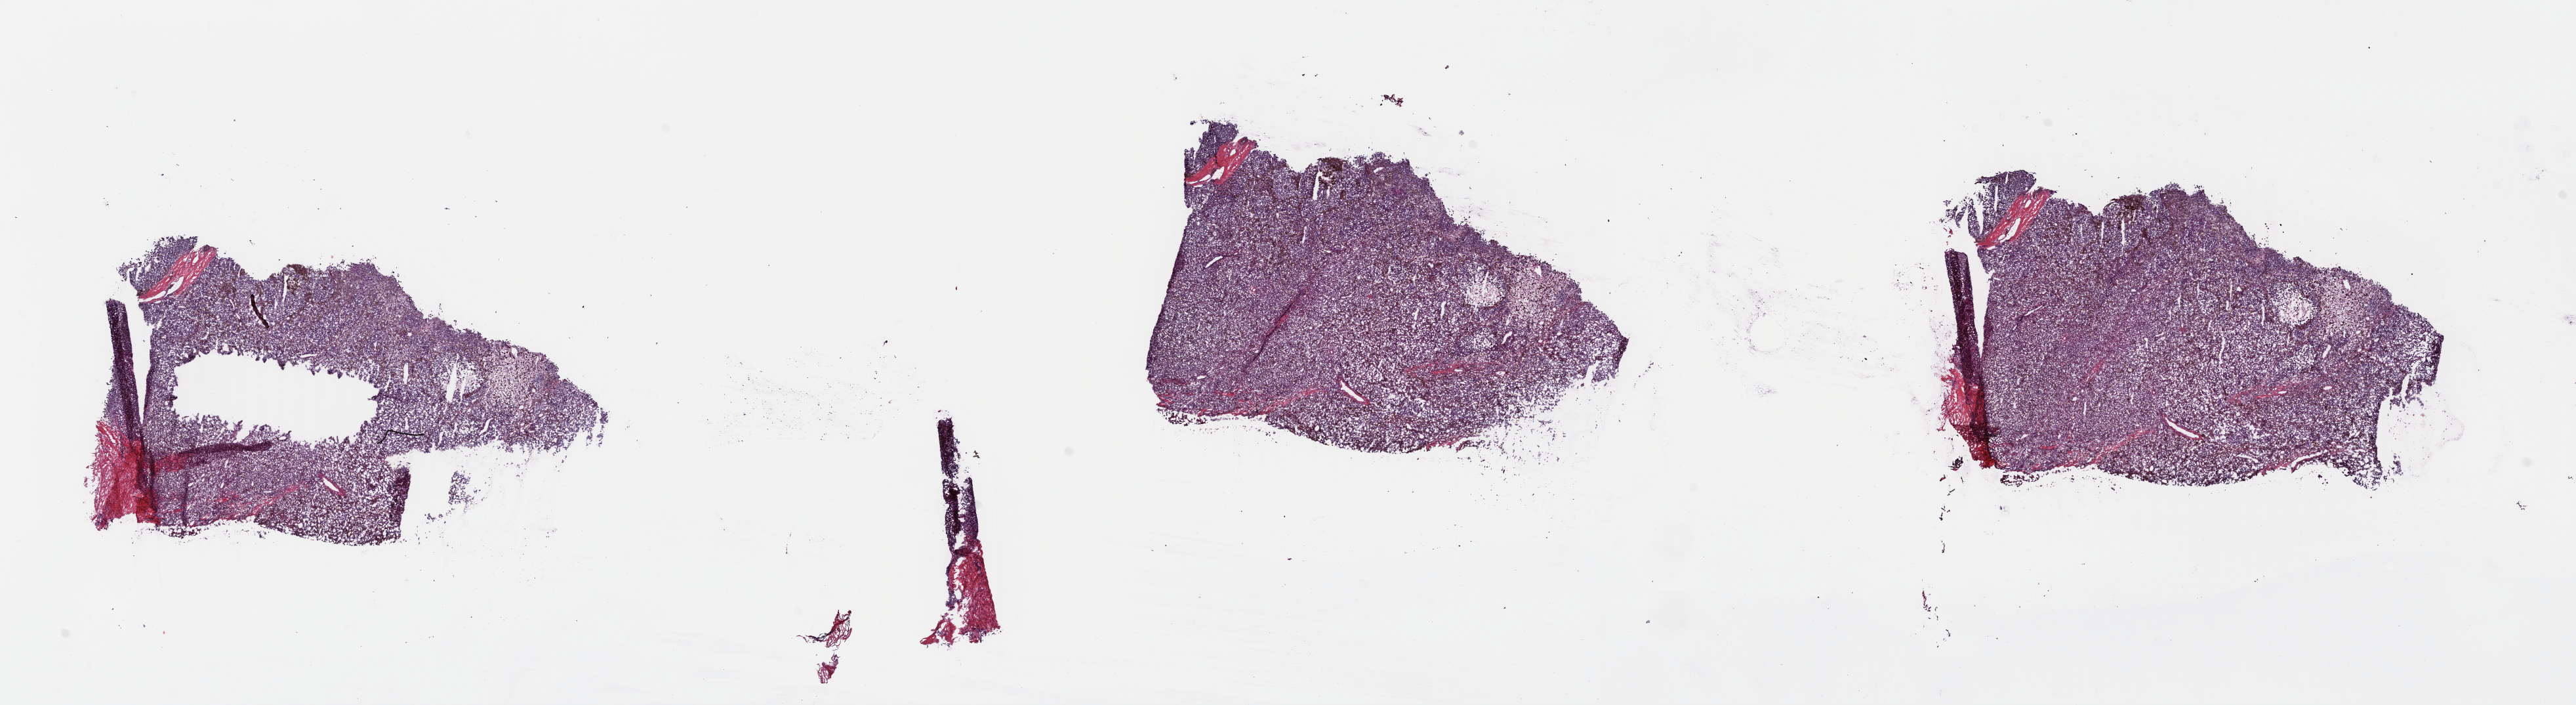
Hematoxylin and eosin (H&E) stained whole-slide image, shown as a low-resolution overview of the whole scanned area (about 30.9 x 8.4 mm, from a 40x scan); frozen section from the top of the tissue portion; sample: primary tumour, skin. Patient: female, age at initial diagnosis 65 years. Slide review estimates, as recorded: tumour cells 99%, tumour nuclei 80%, normal cells 0%, stromal cells 0%, necrosis 1%. Infiltration values recorded for this section: lymphocyte infiltration 2%, monocyte infiltration 0%, neutrophil infiltration 0%.
* diagnosis: Malignant melanoma, NOS